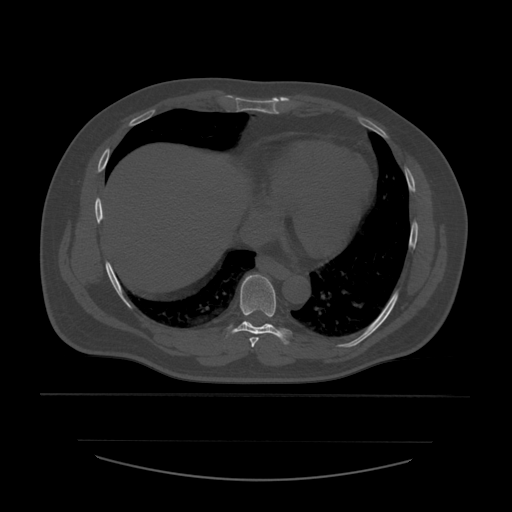
CT including the spine, one axial slice. Reconstruction kernel STANDARD. Bone window (W 1800 / L 400 HU). 1.25 mm slice thickness. 512 × 512 image matrix, field of view 441 × 441 mm. Patient age 44 years. From the clinical record (not read from this slice): primary cancer: soft tissue sarcoma.
Outlined on this slice (semi-automatically segmented with operator editing):
- T7 vertebra: bounding box (x1, y1, x2, y2) in pixels: (250, 337, 260, 348)
- T8 vertebra: (228, 275, 292, 345)